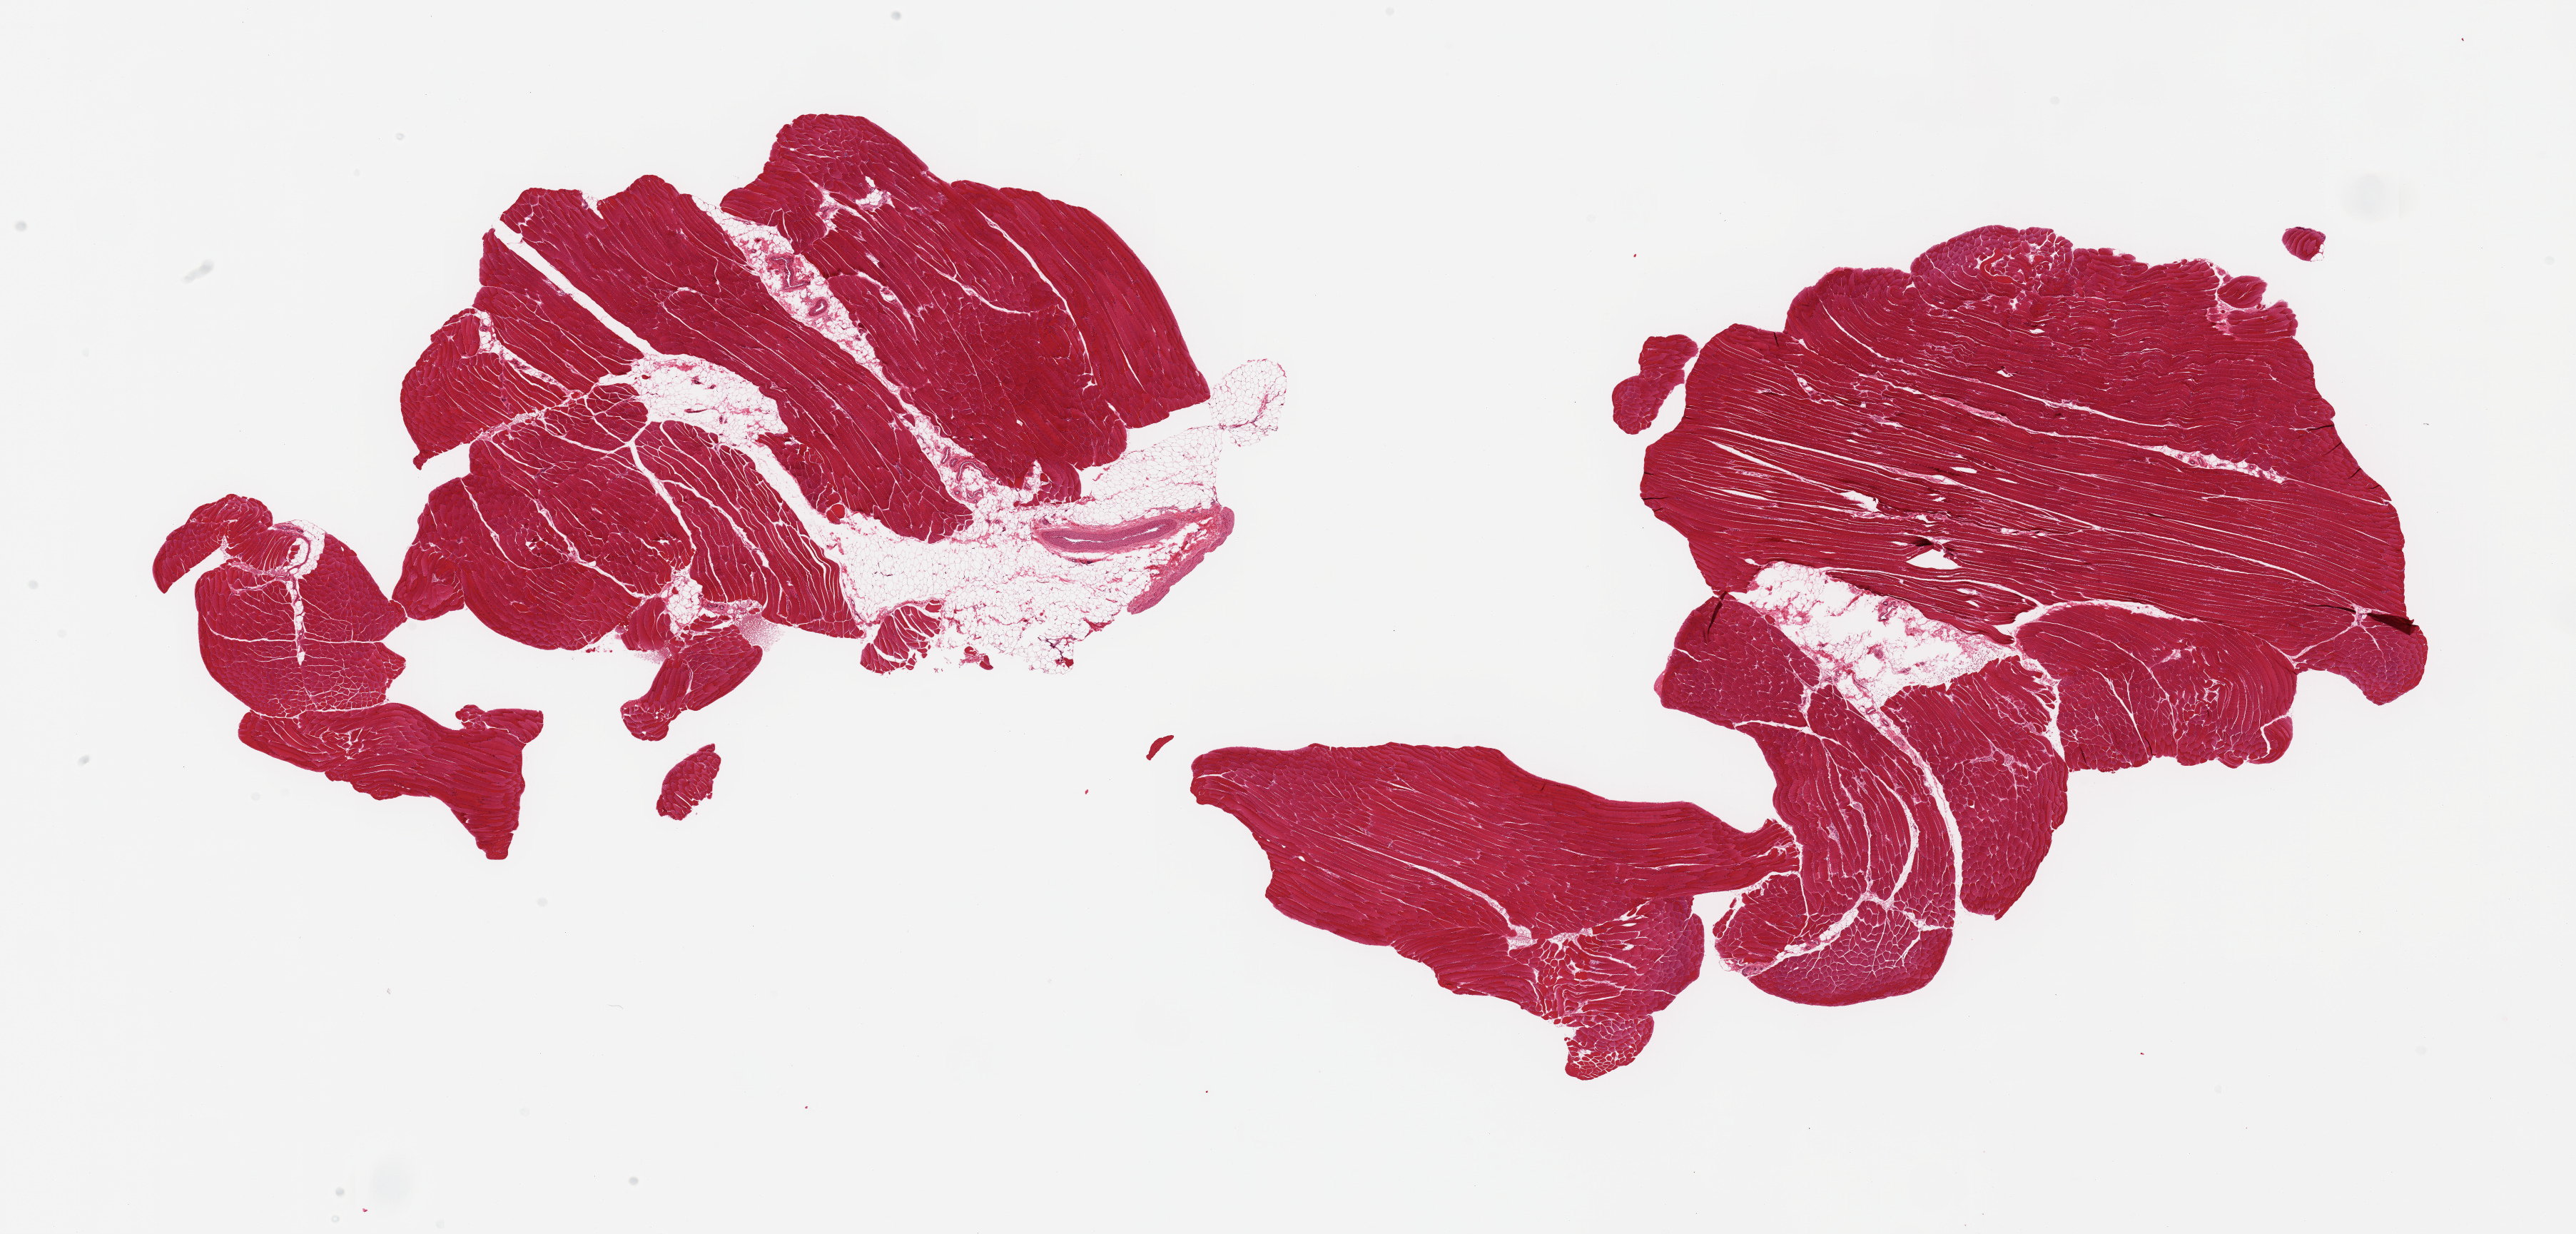
Haematoxylin and eosin whole-slide image — whole scanned area (about 28.5 x 13.7 mm) shown as a low-resolution overview; PAXgene-fixed, paraffin-embedded tissue; sampled site (target tissue): skeletal muscle; tissue donor sample. Donor sex: male.
Review note (as recorded): 2 pieces; skeletal muscle with ~ 5 and 20% internal/external fat.